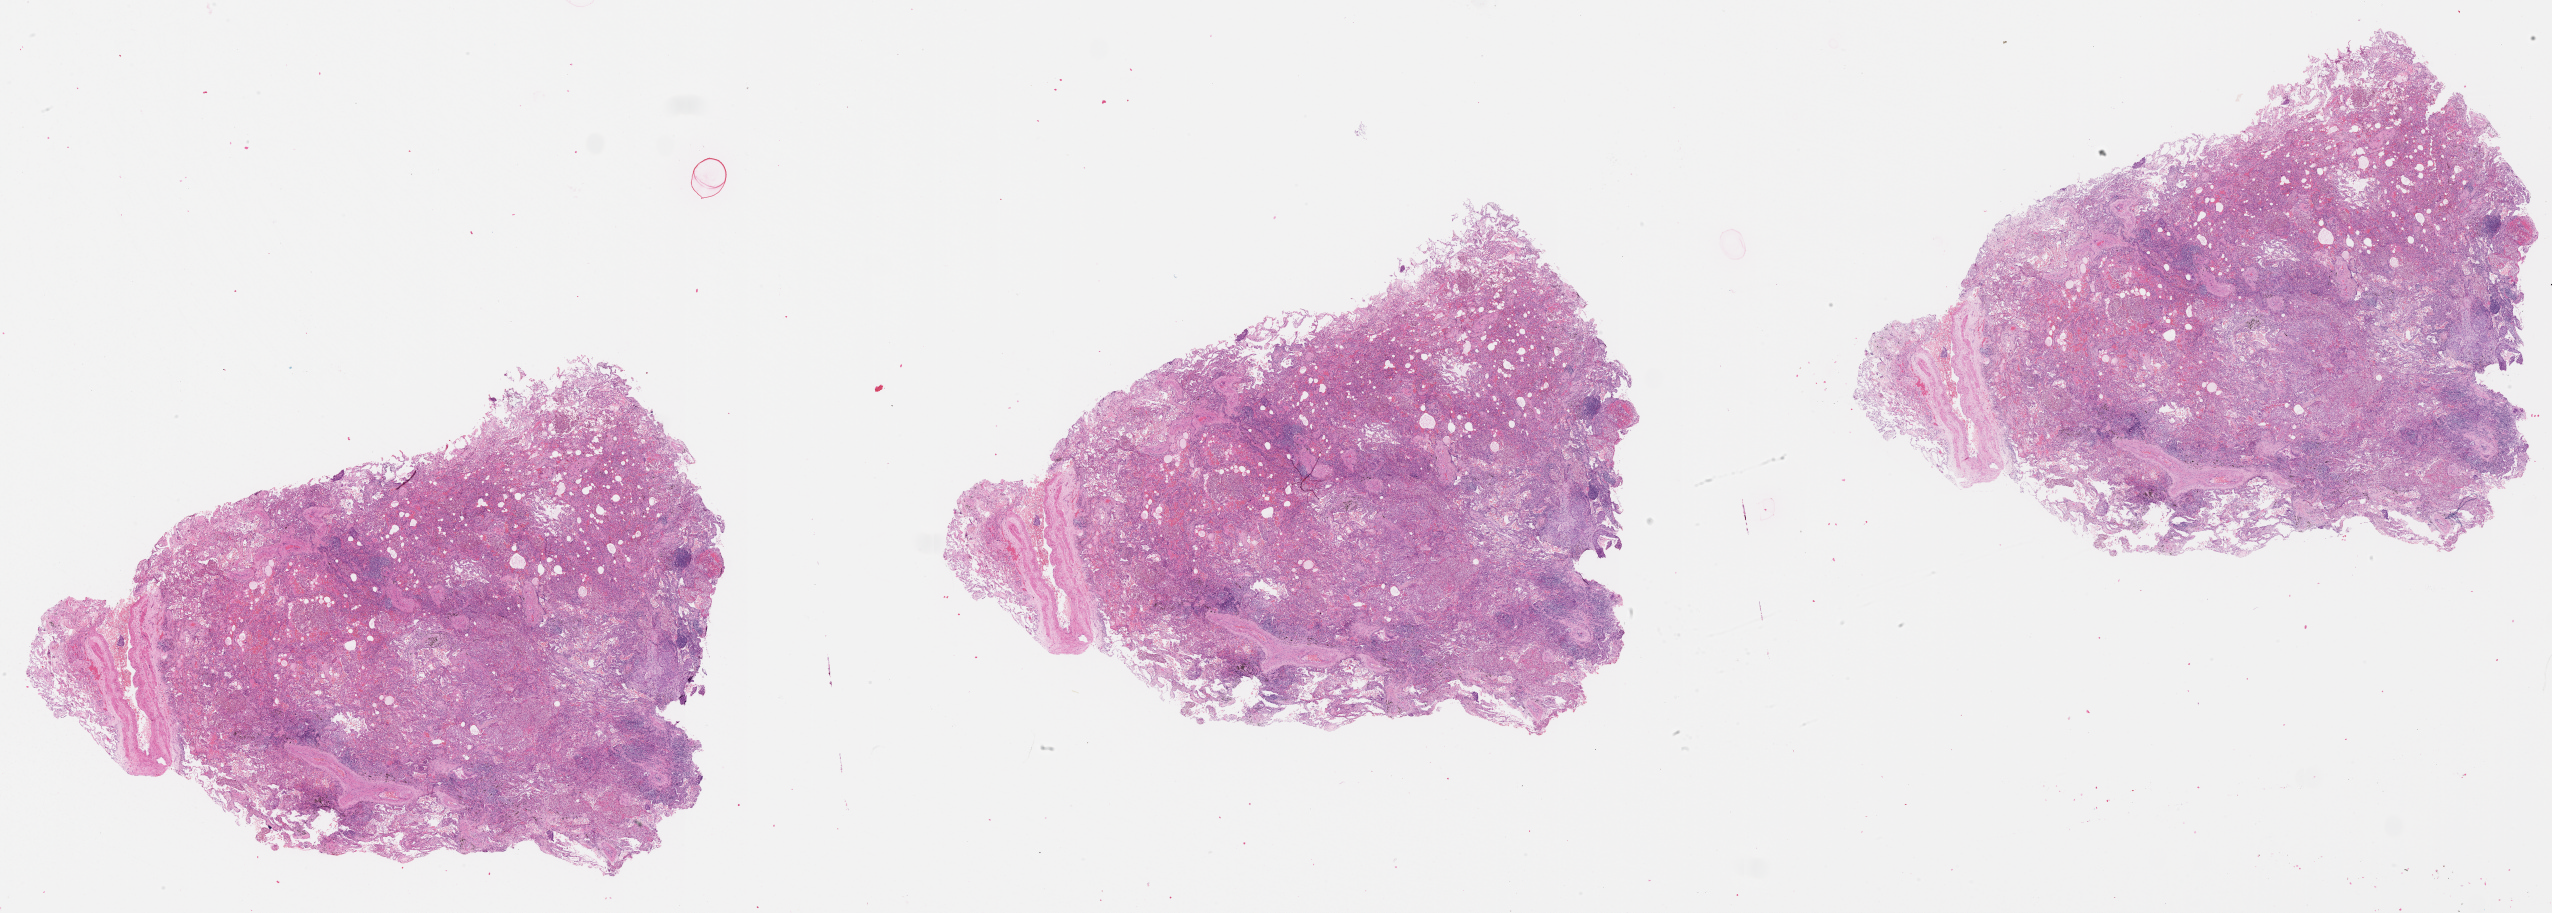
Digitized Hematoxylin and eosin (H&E) stained tissue section (whole slide) — whole scanned area (about 41.1 x 14.7 mm, from a 20x scan) shown as a low-resolution overview; tumour tissue sample, lung. Male, 57 y/o.
Patient diagnosis (cohort enrolment): squamous cell carcinoma (lung).